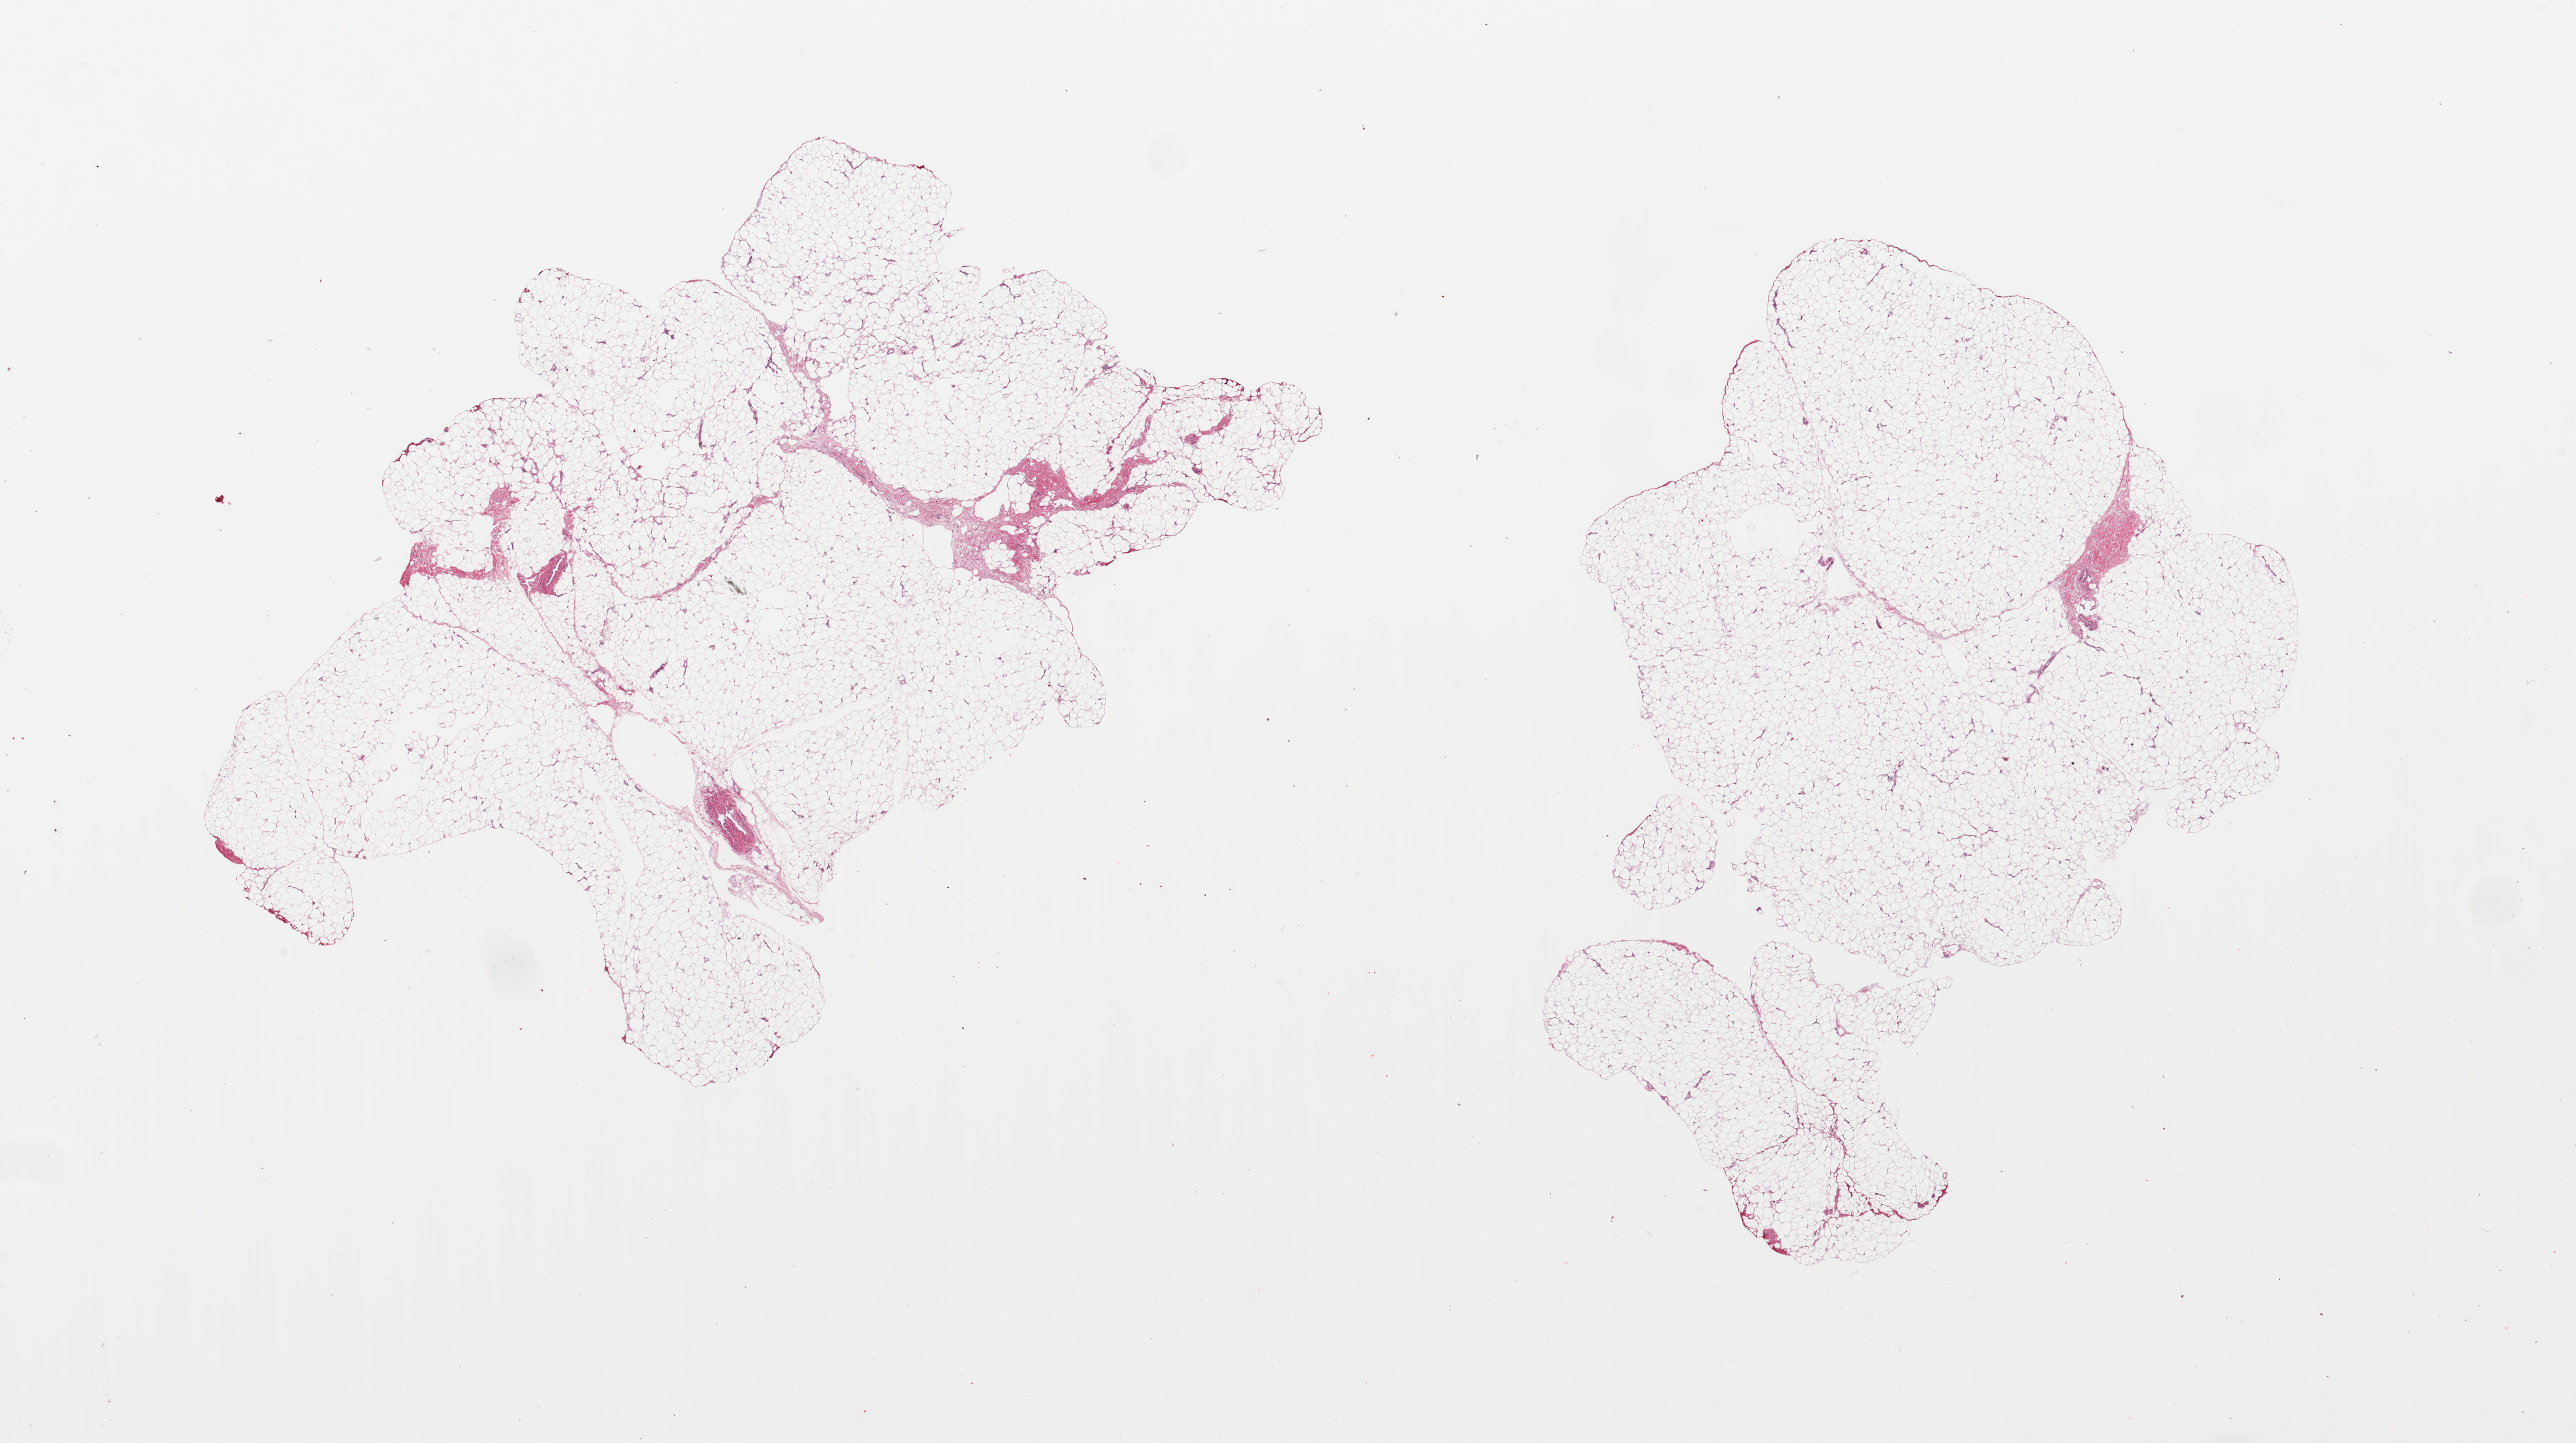
Haematoxylin and eosin whole-slide image, low-resolution overview of the scanned area, about 29.5 x 16.5 mm, PAXgene-fixed, paraffin-embedded tissue, section of adipose tissue (target tissue), donor tissue sample. Donor: male.
Review note (as recorded): 2 pieces; <5% fibrous content.